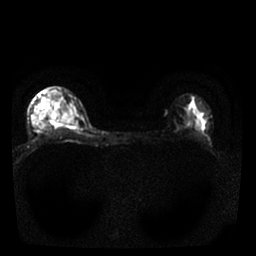
Breast MRI, one axial slice. Slice 19 of 25 in the series (ordered by position). Diffusion-weighted series; image 2 of 4 stored at this slice position (different b-values; order by instance number). 1.5 T. 4 mm slice thickness. 256 × 256 image matrix, field of view 310 × 310 mm. Female patient.
Structures marked on this image (outlined manually by an expert reader):
- tumour on diffusion-weighted imaging: bounding box <51,111,79,125> (left, top, right, bottom; pixels)